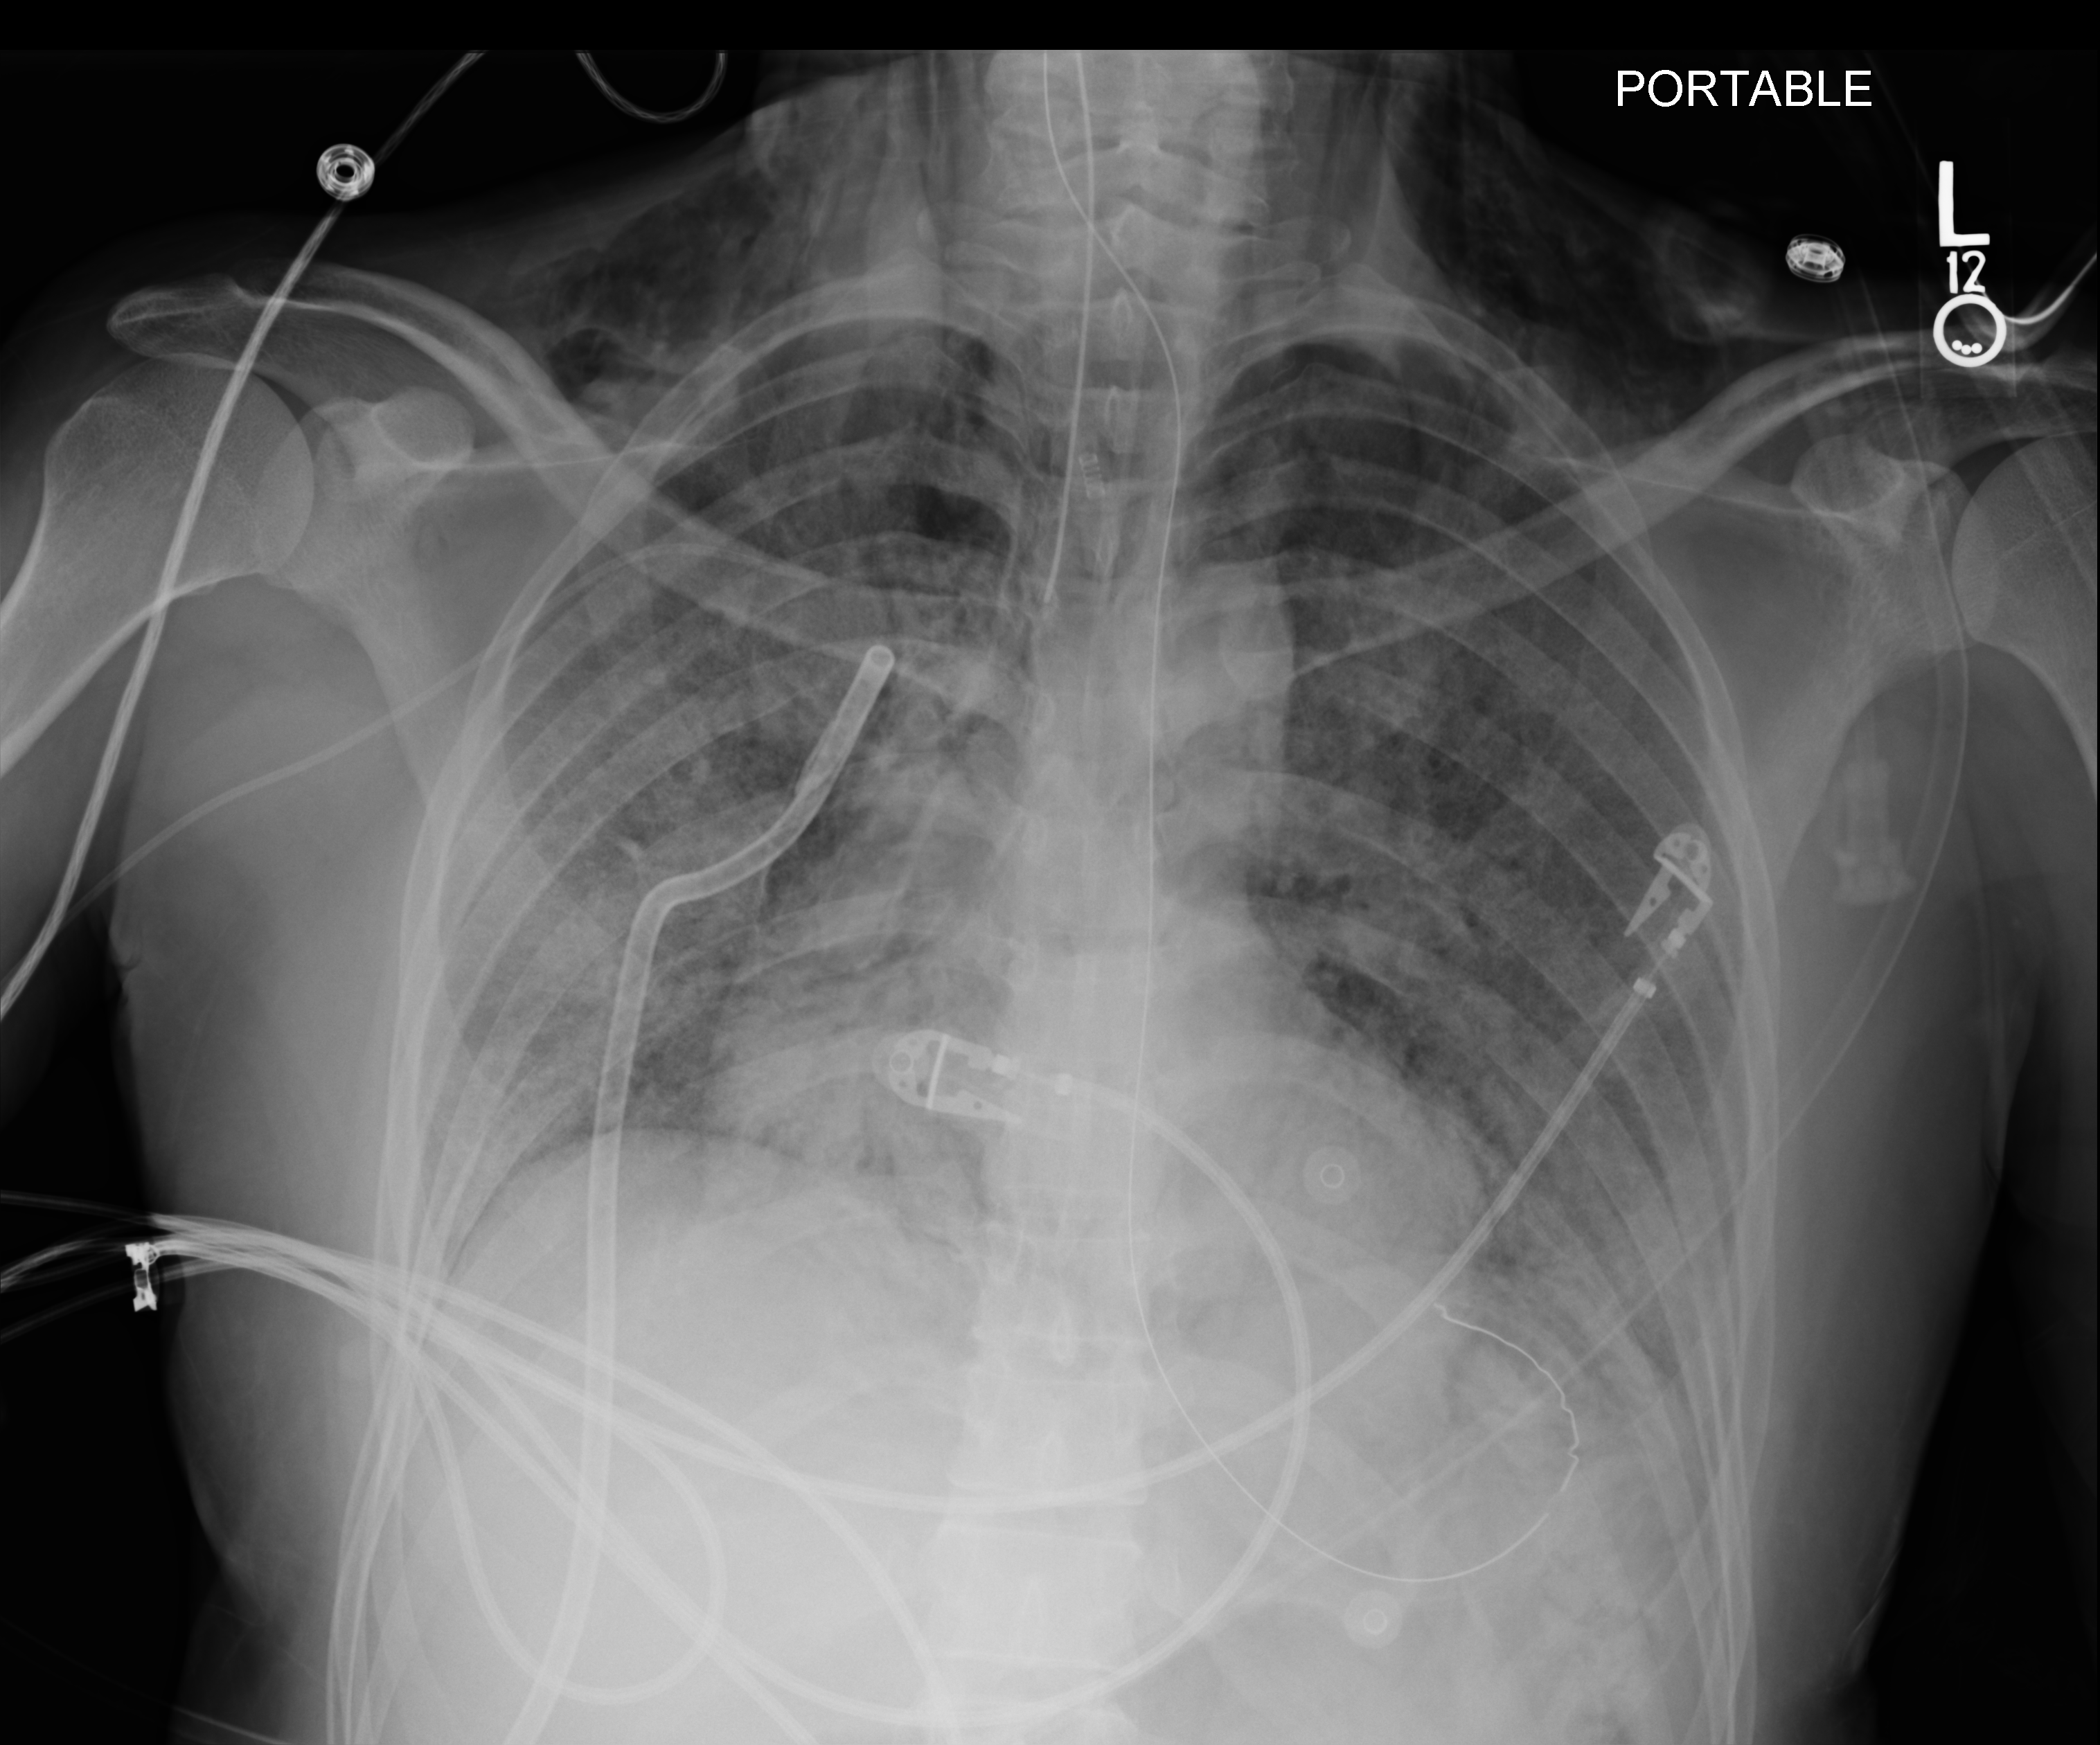
Chest X-ray (portable), anteroposterior (AP) projection. Adult patient hospitalised with COVID-19, age 18–59 years.
From the hospital-stay record, not from the radiograph (when in the stay this image was taken is not recorded): diabetes (admission record): no; admitted to intensive care during this hospital stay: yes; mechanically ventilated during this hospital stay: yes.